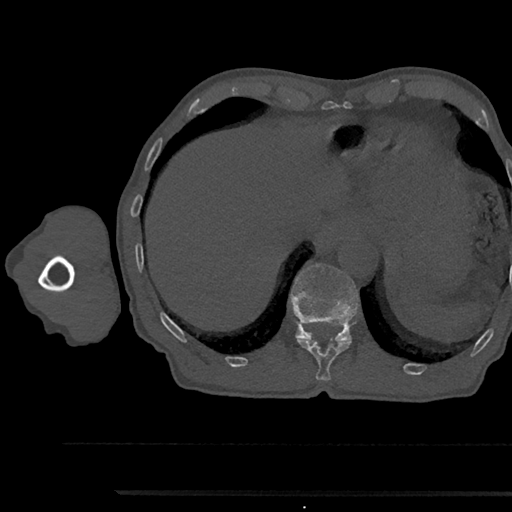
CT including the spine, one axial slice; position 753 of 797 along the scan axis; reconstruction kernel Br40s/3; 120 kVp; bone window (W 1800 / L 400 HU); 0.5 mm slice thickness; 512 × 512 image matrix, field of view 367 × 367 mm. Patient: male, 79 years. From the clinical record (not read from this slice): primary cancer: prostate.
Structures marked on this image (semi-automatically segmented with operator editing):
- T11 vertebra: box from (x=298, y=339) to (x=350, y=381) px
- T12 vertebra: (x=290, y=264)–(x=359, y=342)